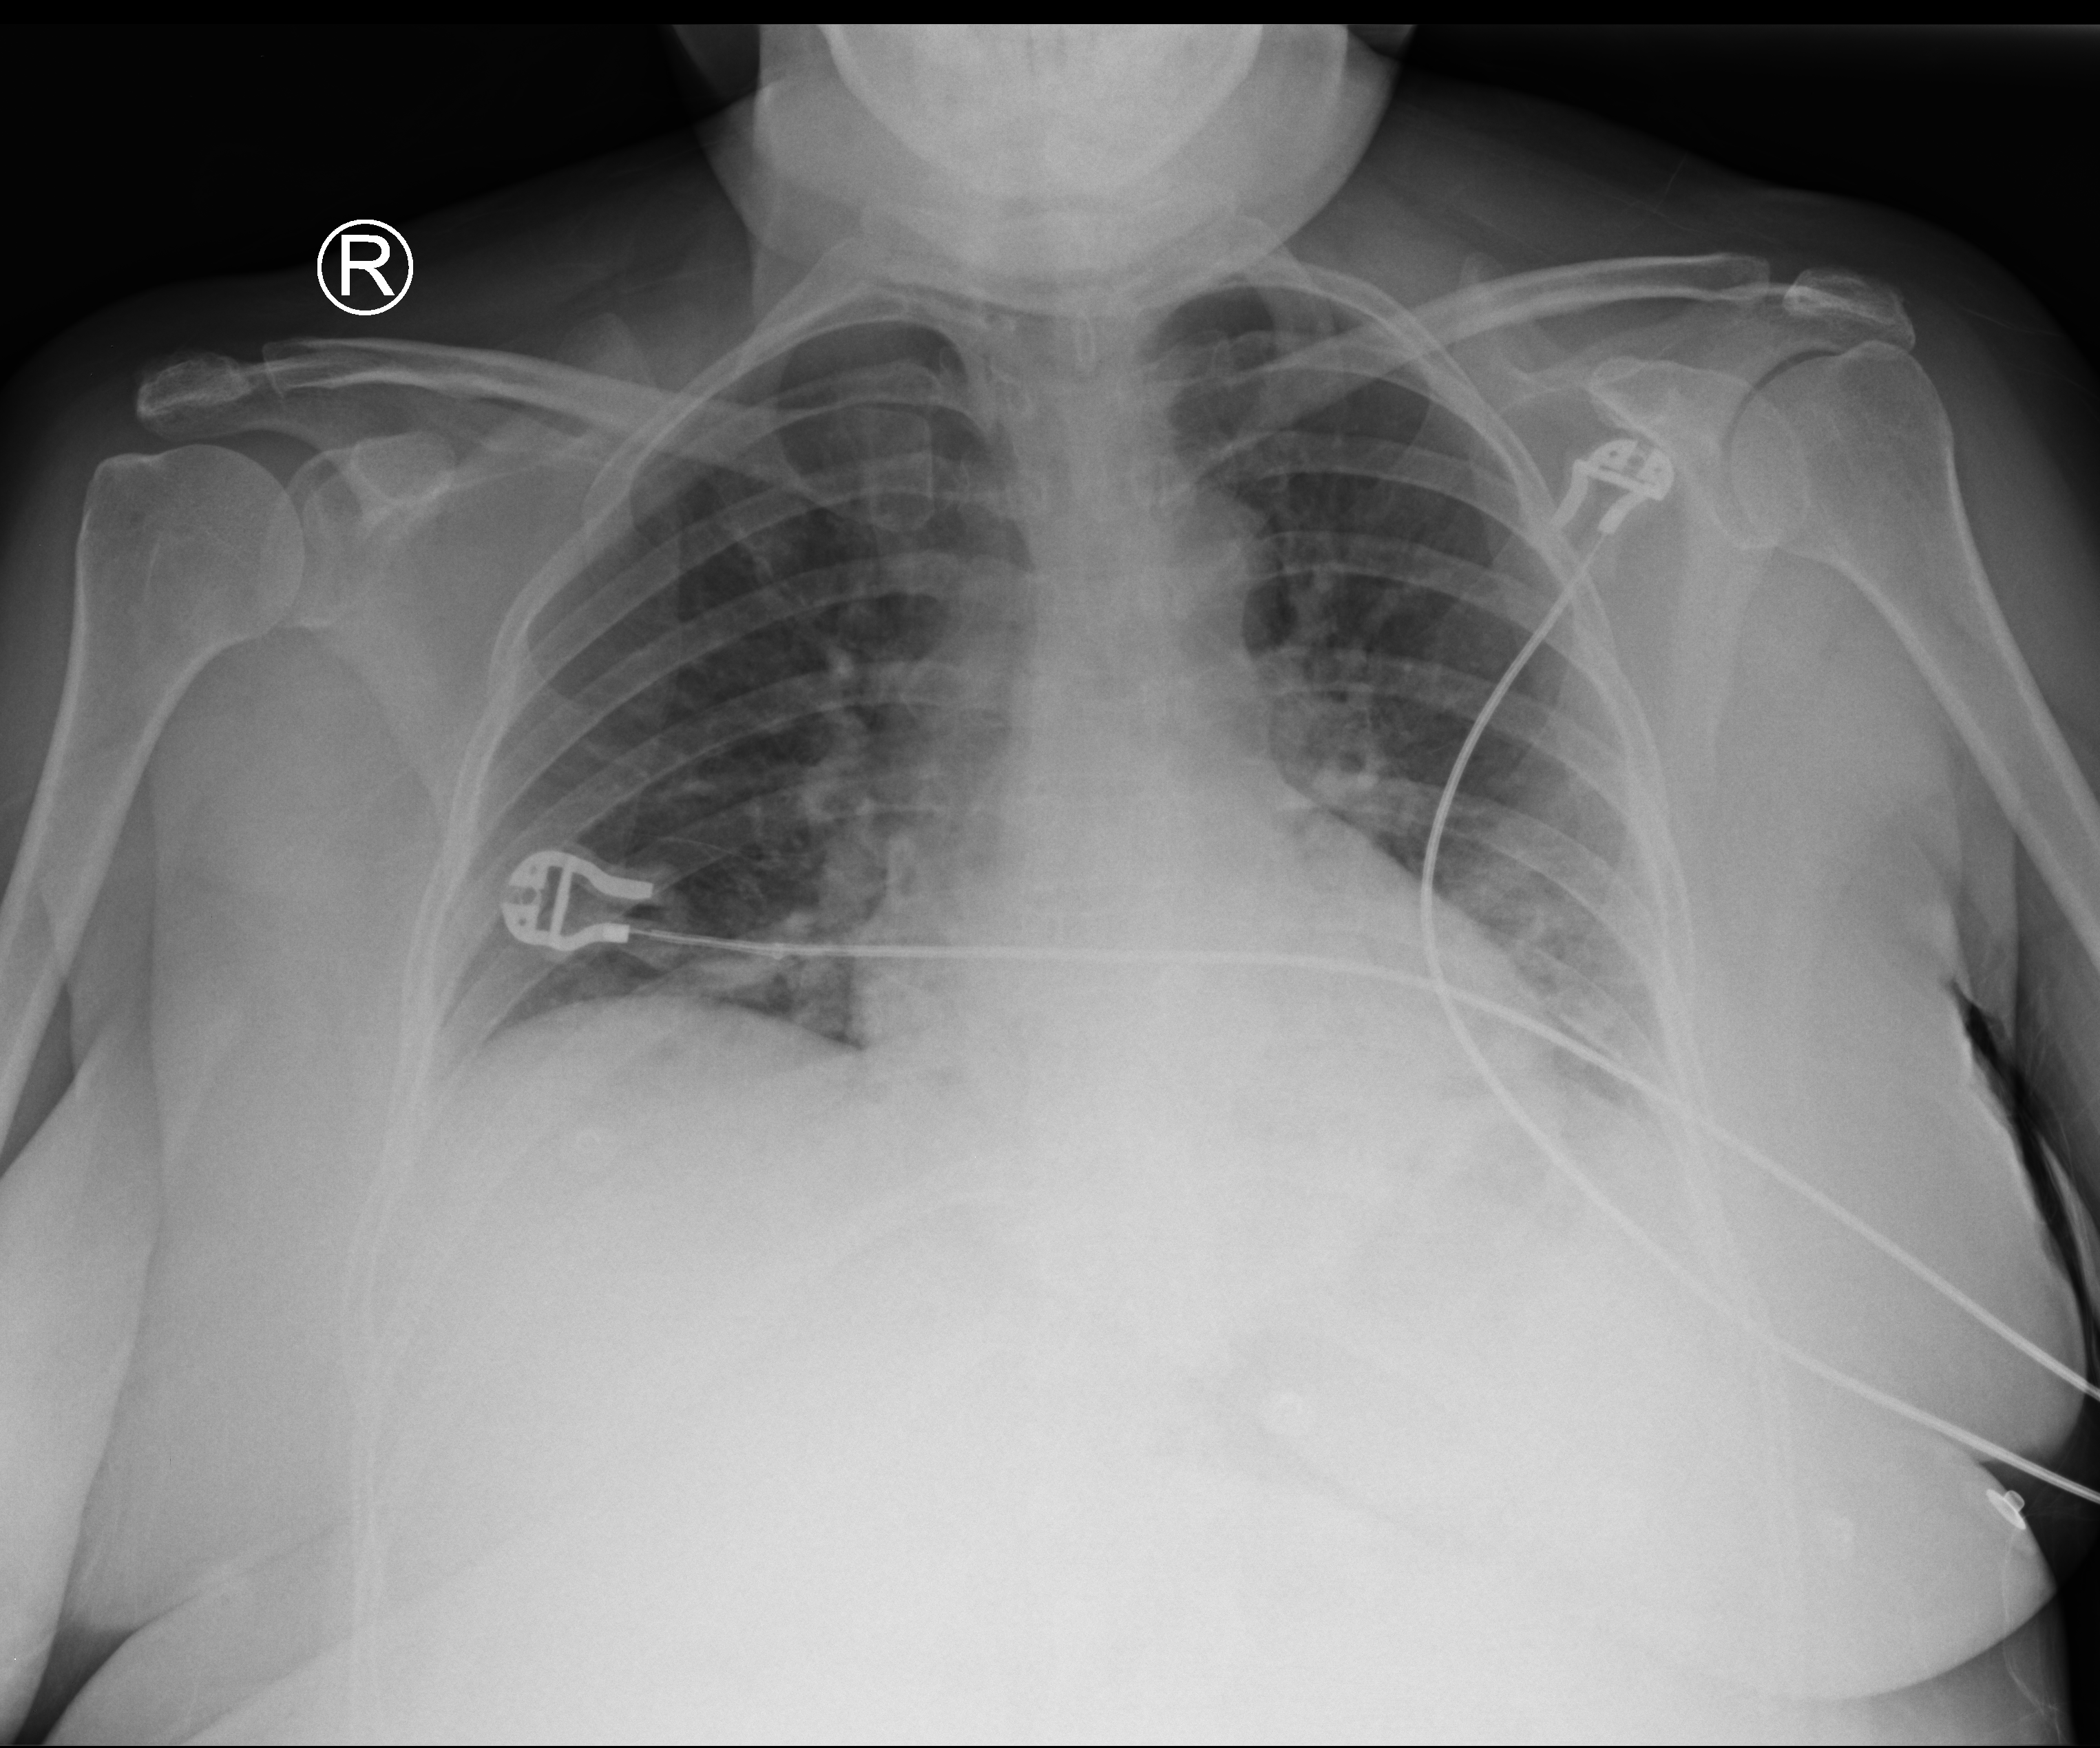
Bedside chest radiograph (computed radiography); anteroposterior (AP) projection. Patient hospitalised with COVID-19; female, aged 18–59 years.
From the hospital-stay record, not from the radiograph (when in the stay this image was taken is not recorded):
- admitted to intensive care during this hospital stay: no